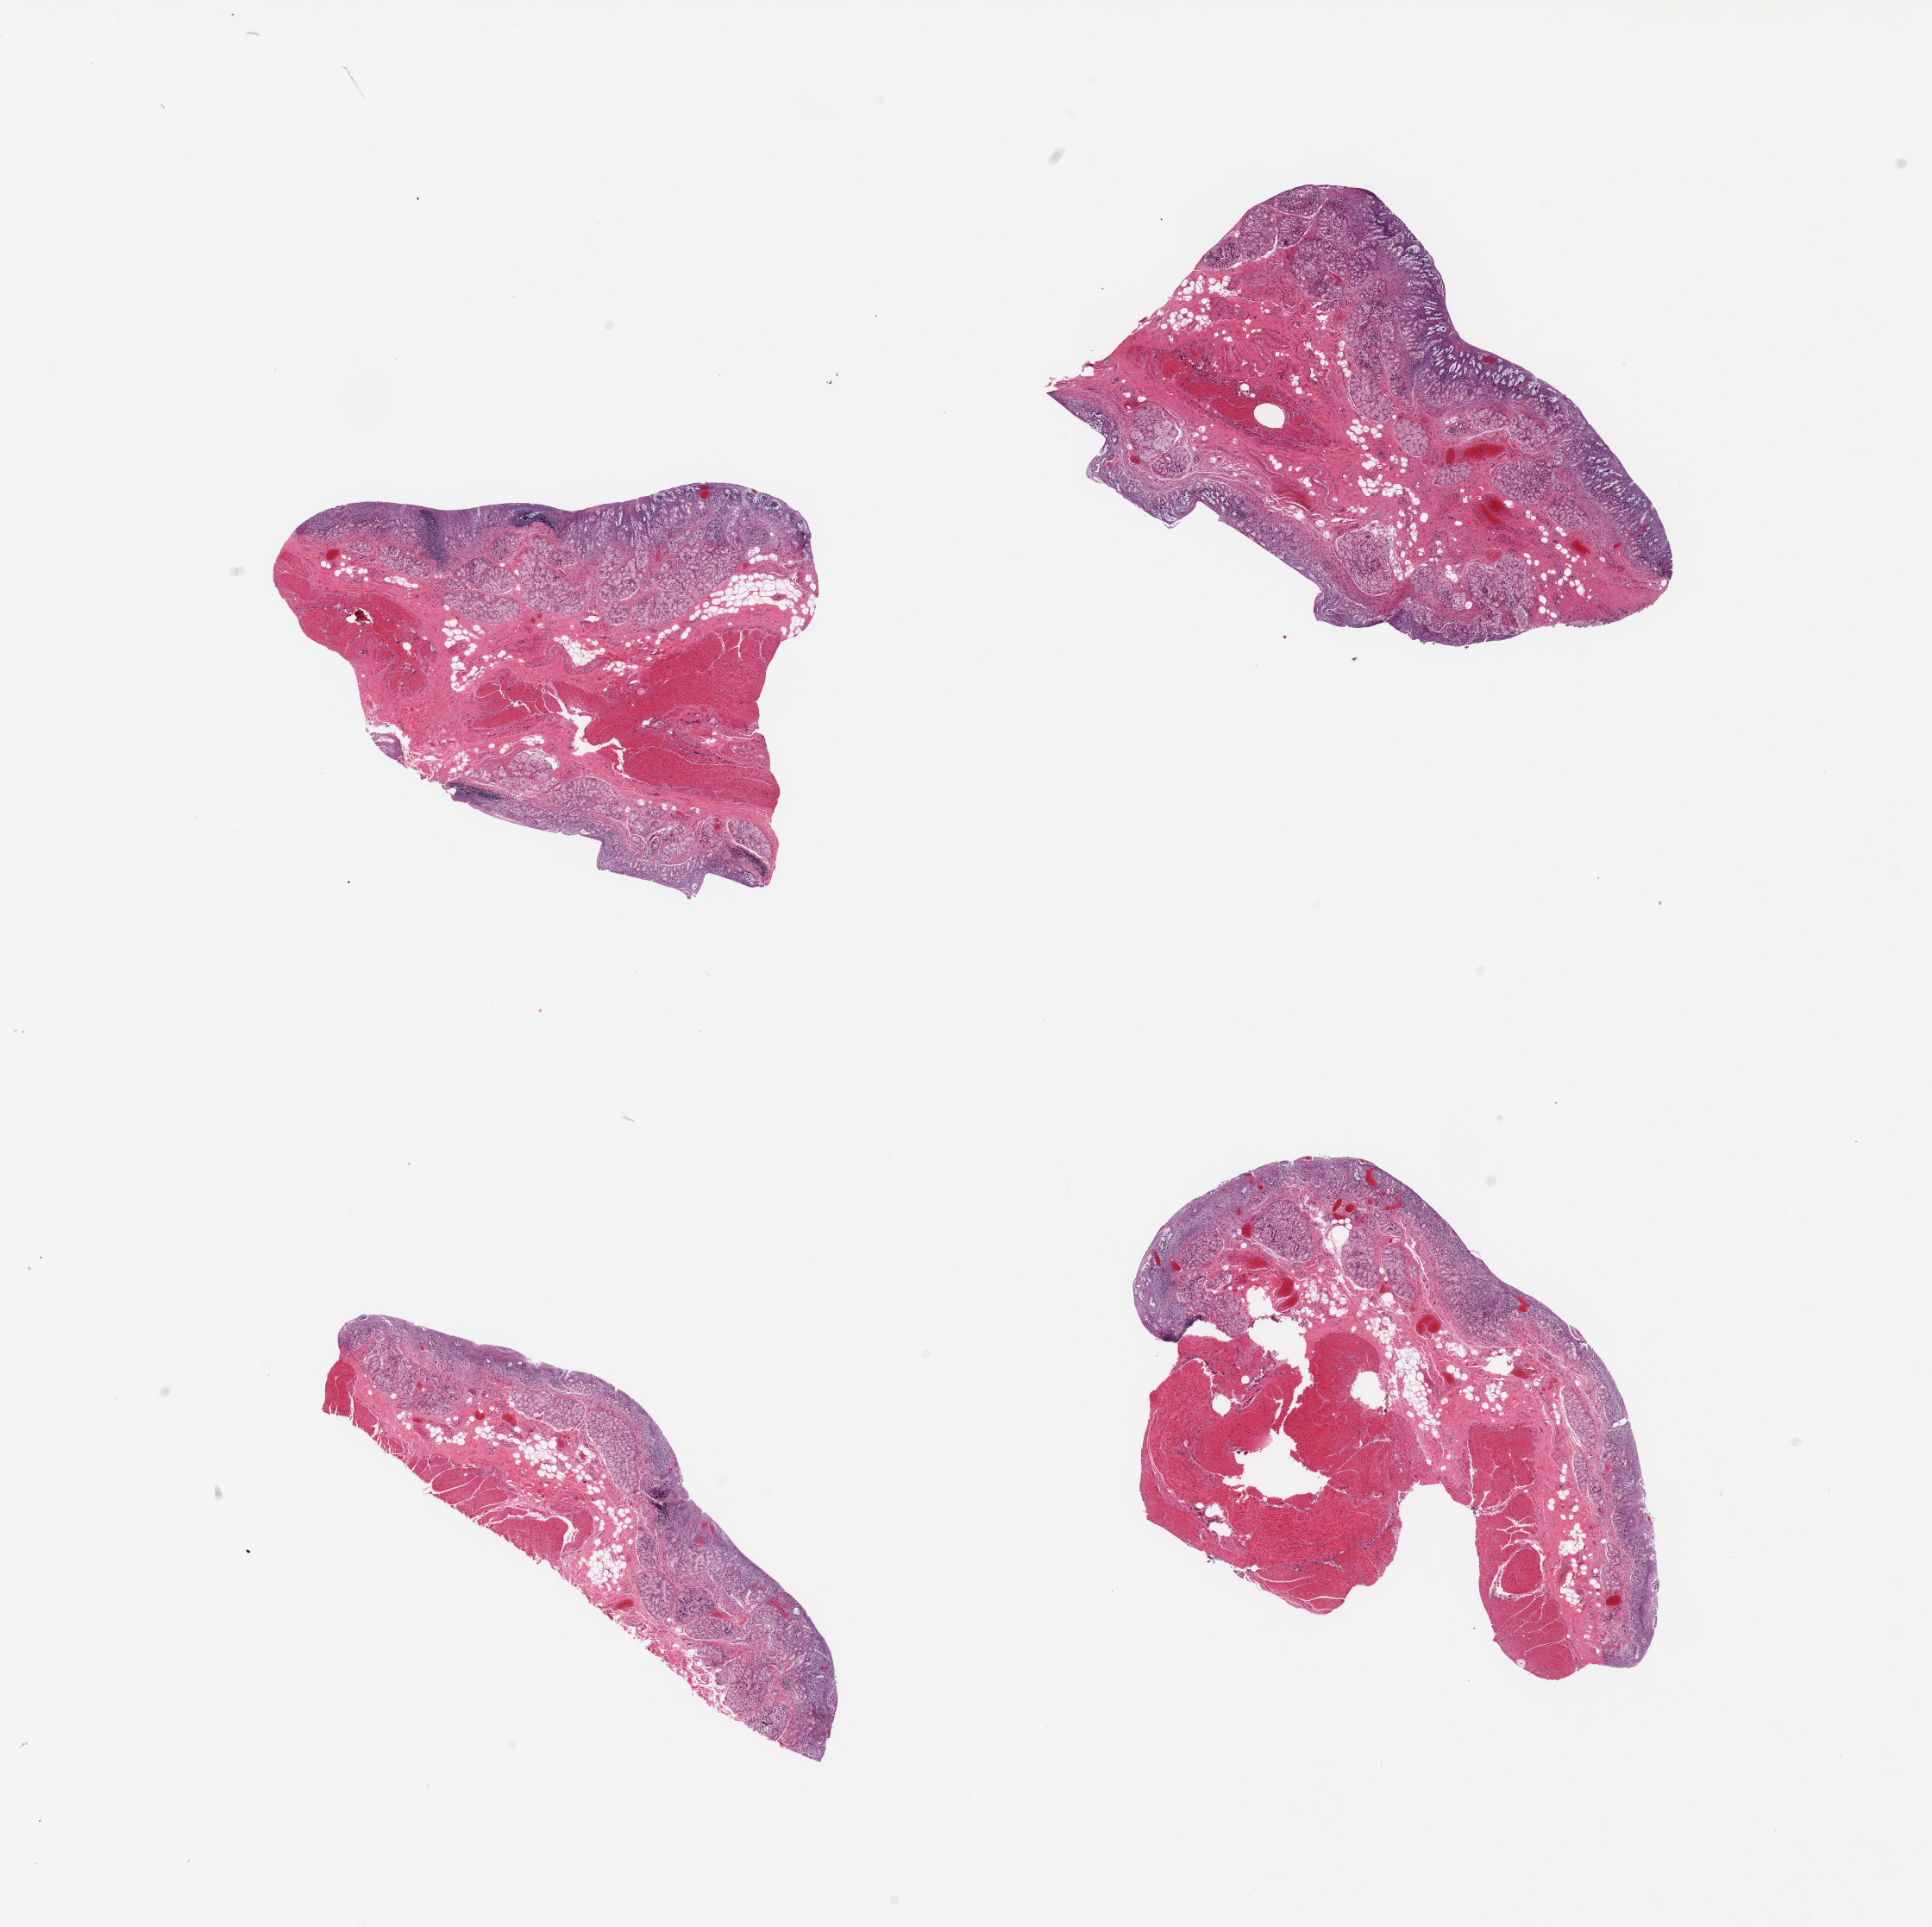
Digitized haematoxylin and eosin-stained section, brightfield — shown as a low-resolution overview of the whole scanned area (about 17.7 x 17.7 mm), PAXgene-fixed paraffin-embedded (PFPE) section, section of stomach (target tissue), tissue donor sample. Male donor.
* review note (as recorded): 4 pieces; antral rather than body mucosa sampled